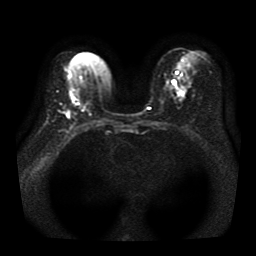
Breast MRI, one axial slice; slice 20 of 41 in the series (ordered by position); diffusion-weighted series; image 2 of 4 stored at this slice position (different b-values; order by instance number); 1.5 T; 256 × 256 image matrix, field of view 330 × 330 mm. Female patient.
Outlined on this slice (outlined manually by an expert reader):
- tumour on diffusion-weighted imaging: bounding box (x1, y1, x2, y2) in pixels: (63, 107, 72, 115)